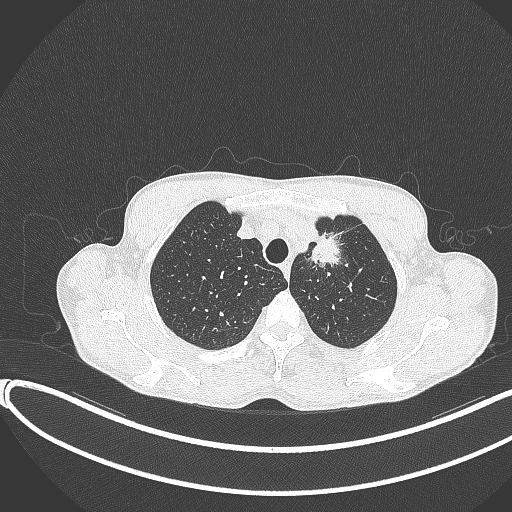
Chest CT, one axial slice; slice 320 of 374 in the series (ordered by position); reconstruction kernel B70f; 120 kVp; lung window (W 1500 / L -600 HU); 1 mm slice thickness; 512 × 512 image matrix, field of view 400 × 400 mm. Male patient, age 58 years. Case-level facts recorded for this patient, not image findings: clinical TNM (as recorded): T1c N1 M0.
Outlined on this slice (rectangle marked by the reading radiologist):
- lung tumour (recorded histology: adenocarcinoma): box from (x=308, y=230) to (x=348, y=280) px